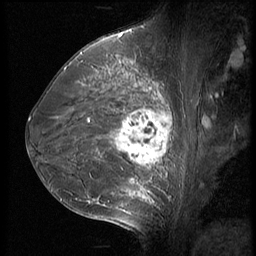
Breast MRI (dynamic contrast-enhanced), one sagittal slice. 3 images stored at this slice position (order not interpretable as contrast timing). 1.5 T. TE 4.2 ms, TR 9 ms. 2.5 mm slice thickness. 256 × 256 image matrix, field of view 180 × 180 mm. Patient: female, 35 years. Case-level facts recorded for this patient, not image findings: setting: breast cancer imaged before/during neoadjuvant chemotherapy; receptor status: HR-positive, HER2-negative.
Outlined on this slice (semi-automatic segmentation, software-assisted and operator-edited):
- analysis volume of interest (the breast-tissue region the enhancement analysis was run in; not a lesion): box from (x=63, y=60) to (x=190, y=218) px
- tumour enhancement mask (voxels above the 140 % enhancement threshold inside the analysis volume of interest): (x=100, y=78)–(x=172, y=214)